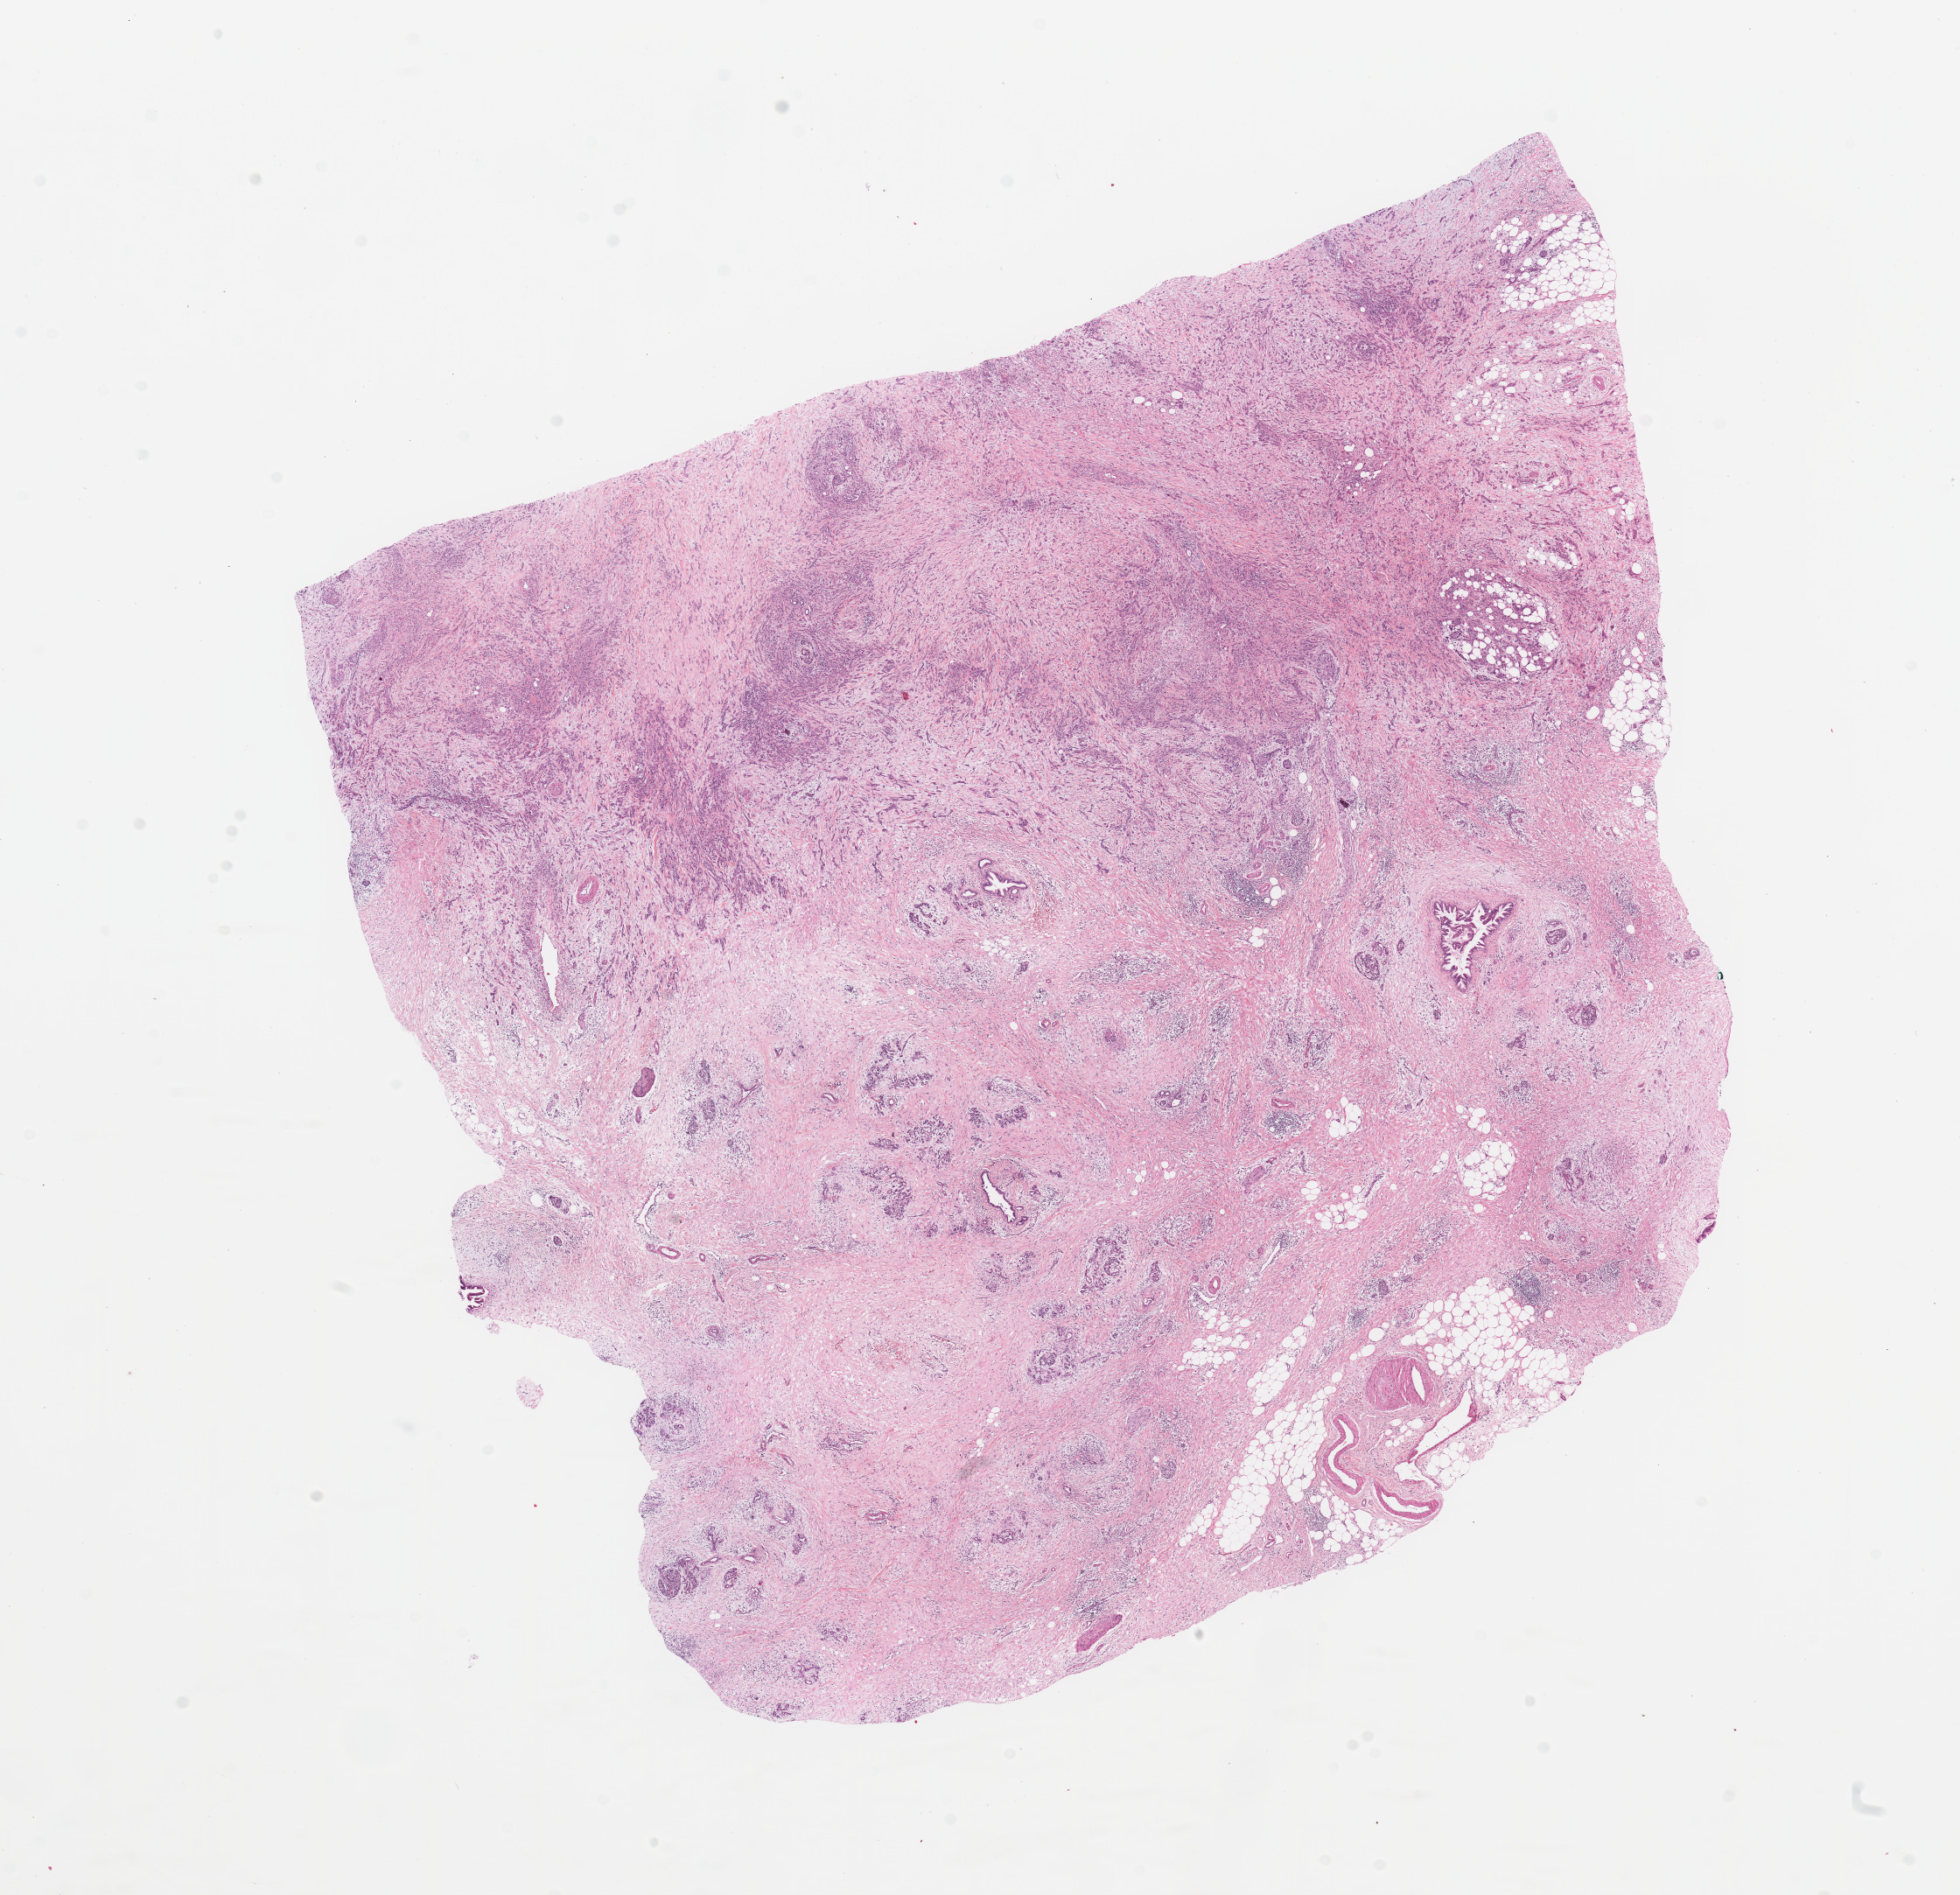
Whole-slide histology image, H&E-stained, low-resolution overview of the scanned area, about 17.7 x 17.1 mm (slide scanned at 20x), tumour tissue sample, pancreas. Female, 60 y/o.
Diagnosis: Infiltrating duct carcinoma, NOS.